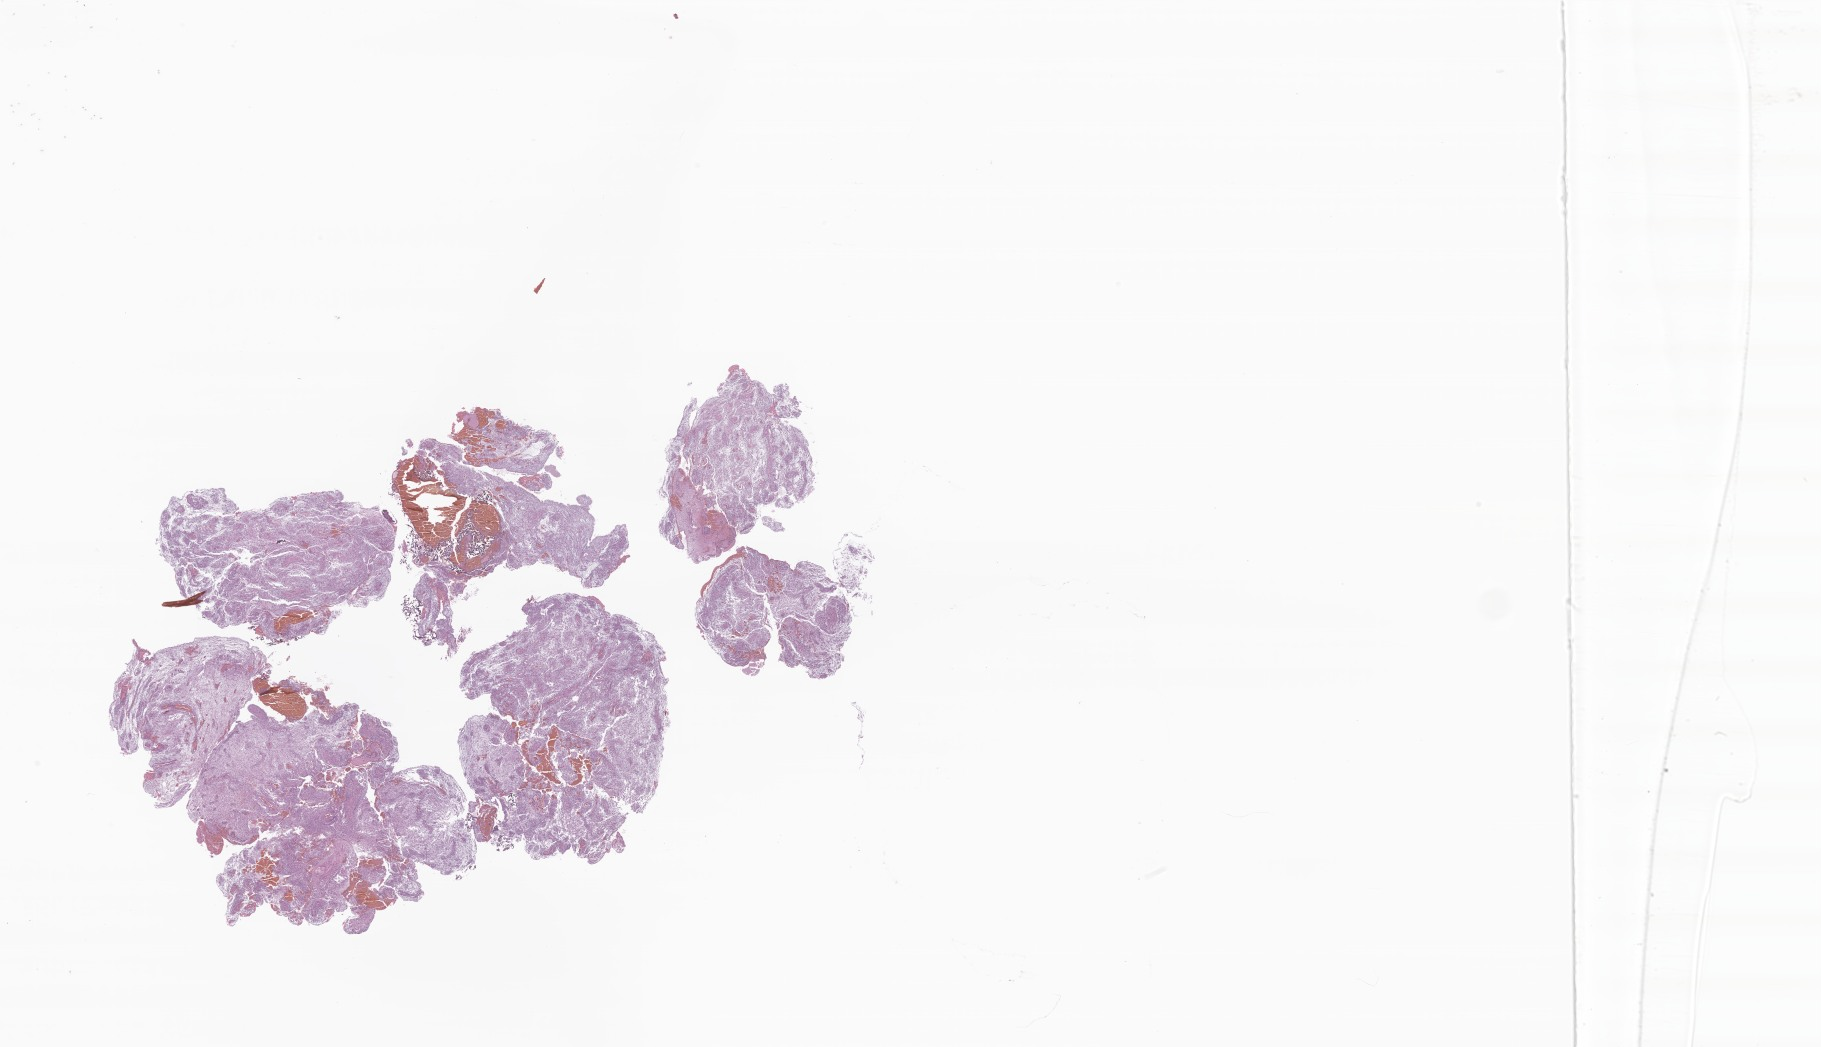
Whole-slide image, H&E stain of tumor tissue from the cerebellum — shown as a low-resolution overview of the whole scanned area (about 30.7 x 17.7 mm); formalin-fixed paraffin-embedded section. Male patient, age 74 months.
Diagnosis (ICD-O-3 morphology term): Pilocytic astrocytoma.